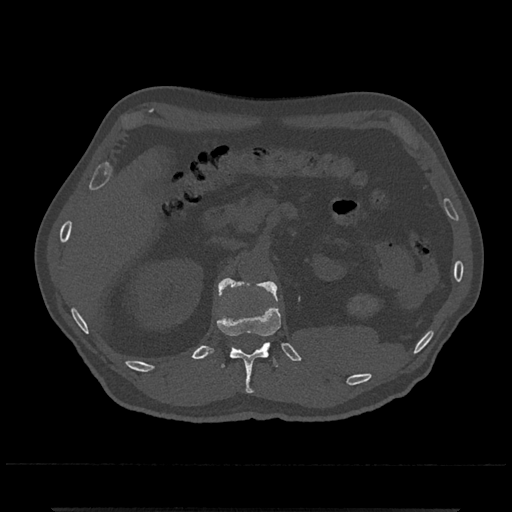
CT including the spine, one axial slice. Slice 413 of 797 in the series (ordered by position). Reconstruction kernel Br40s/3. Bone window (W 1800 / L 400 HU). 512 × 512 image matrix. Patient: male, 67 years. From the clinical record (not read from this slice): primary cancer: prostate.
Structures marked on this image (semi-automatic segmentation, software-assisted and operator-edited):
- L1 vertebra: bounding box [x1, y1, x2, y2] px = [218, 278, 278, 301]
- T12 vertebra: [217, 306, 281, 394]